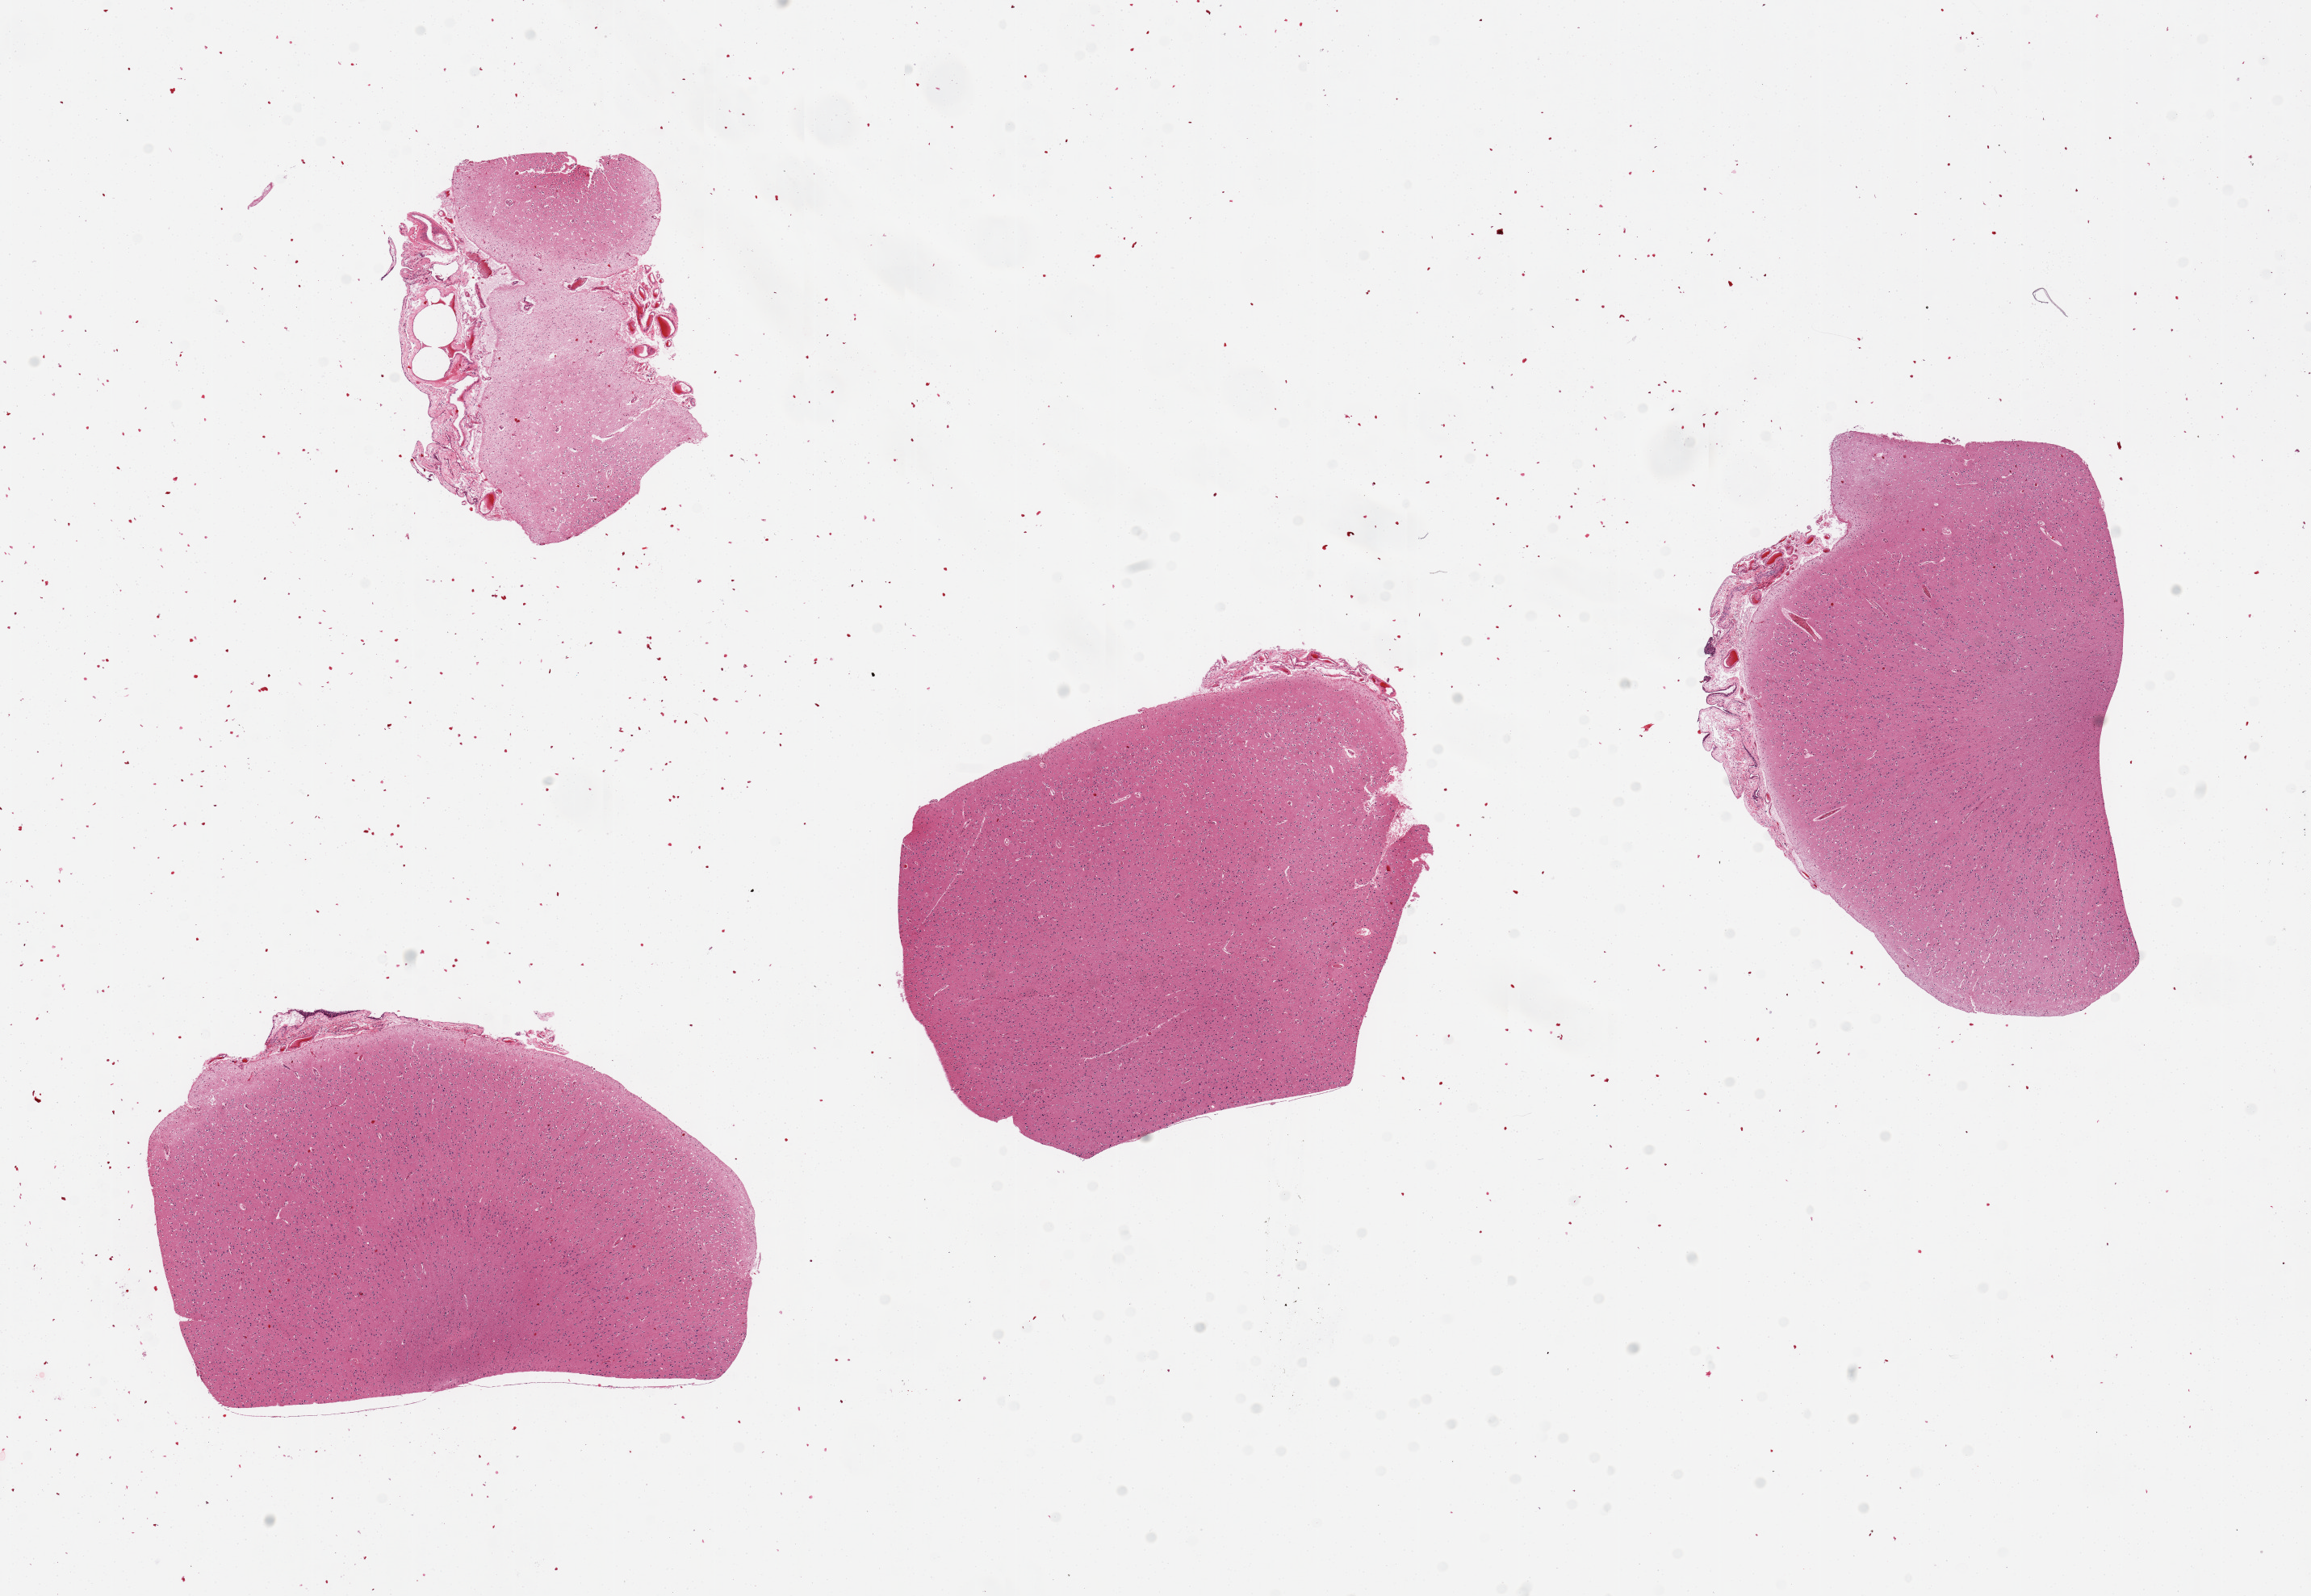
Whole-slide image, haematoxylin and eosin stain, shown as a low-resolution overview of the whole scanned area (about 22.6 x 15.6 mm). PAXgene-fixed paraffin-embedded (PFPE) section. Target tissue: cerebral cortex. Tissue donor sample. Donor sex: male.
- review note (as recorded): 4 pieces, adherent meninges